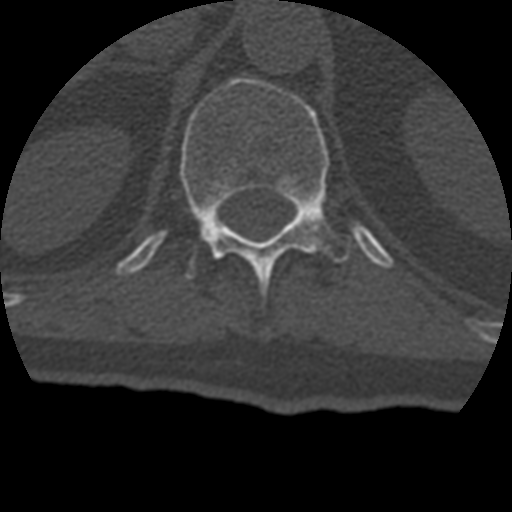
CT including the spine, one axial slice; position 171 of 399 along the scan axis; 120 kVp; bone window (W 1800 / L 400 HU); 512 × 512 image matrix, field of view 160 × 160 mm. Patient age 69 years. Case-level facts recorded for this patient, not image findings: primary cancer: prostate.
Outlined on this slice (semi-automatically segmented with operator editing):
- T12 vertebra: bounding box [x1, y1, x2, y2] px = [180, 76, 350, 286]